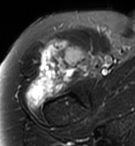
MRI of an extremity soft-tissue mass, one axial slice; slice 77 of 95 in the series (ordered by position); T2-weighted fat-saturated; MR volume resampled by the dataset authors to the PET/CT grid (not the native acquisition matrix); 3.27 mm slice thickness; 135 × 146 image matrix, field of view 132 × 143 mm. Female patient. Case-level facts recorded for this patient, not image findings: histological type: pleiomorphic undifferentiated sarcoma; grade: high; site of the primary tumour: right quadricep.
Structures marked on this image (expert contour drawn on MRI and transferred to this co-registered scan by the dataset authors):
- gross tumour volume including surrounding oedema: bounding box [x1, y1, x2, y2] px = [26, 38, 93, 105]
- gross tumour volume (mass): [28, 38, 93, 103]